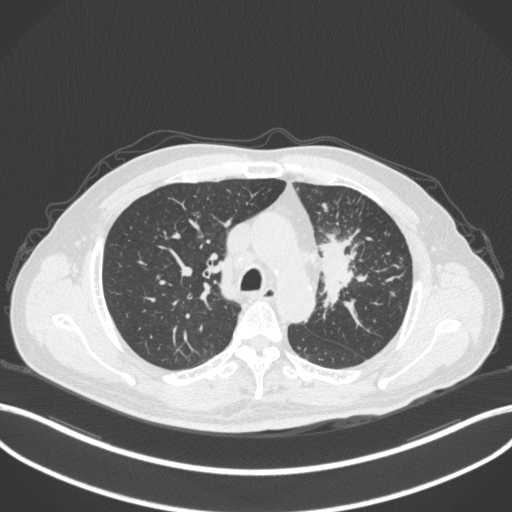
Chest CT, one axial slice; reconstruction kernel B31f; 120 kVp; lung window (W 1500 / L -600 HU); 1 mm slice thickness; 512 × 512 image matrix, field of view 400 × 400 mm. Patient: male, 69 years. From the clinical record (not read from this slice): clinical TNM (as recorded): T2a N2 M0; histopathological grade: G2-3.
Annotated regions visible in this slice (bounding box drawn by a radiologist):
- lung tumour (recorded histology: adenocarcinoma): bounding box <316,228,360,309> (left, top, right, bottom; pixels)